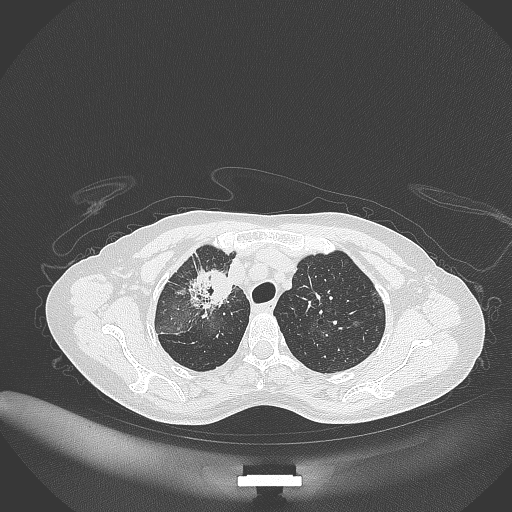
Chest CT, one axial slice; slice 259 of 284 in the series (ordered by position); lung window (W 1500 / L -600 HU); 1 mm slice thickness; 512 × 512 image matrix, field of view 400 × 400 mm. Female patient, age 59 years. From the clinical record (not read from this slice): clinical TNM (as recorded): T3 N0 M0; histopathological grade: G1.
Outlined on this slice (rectangle marked by the reading radiologist):
- lung tumour (recorded histology: adenocarcinoma): bounding box [x1, y1, x2, y2] px = [184, 261, 234, 311]